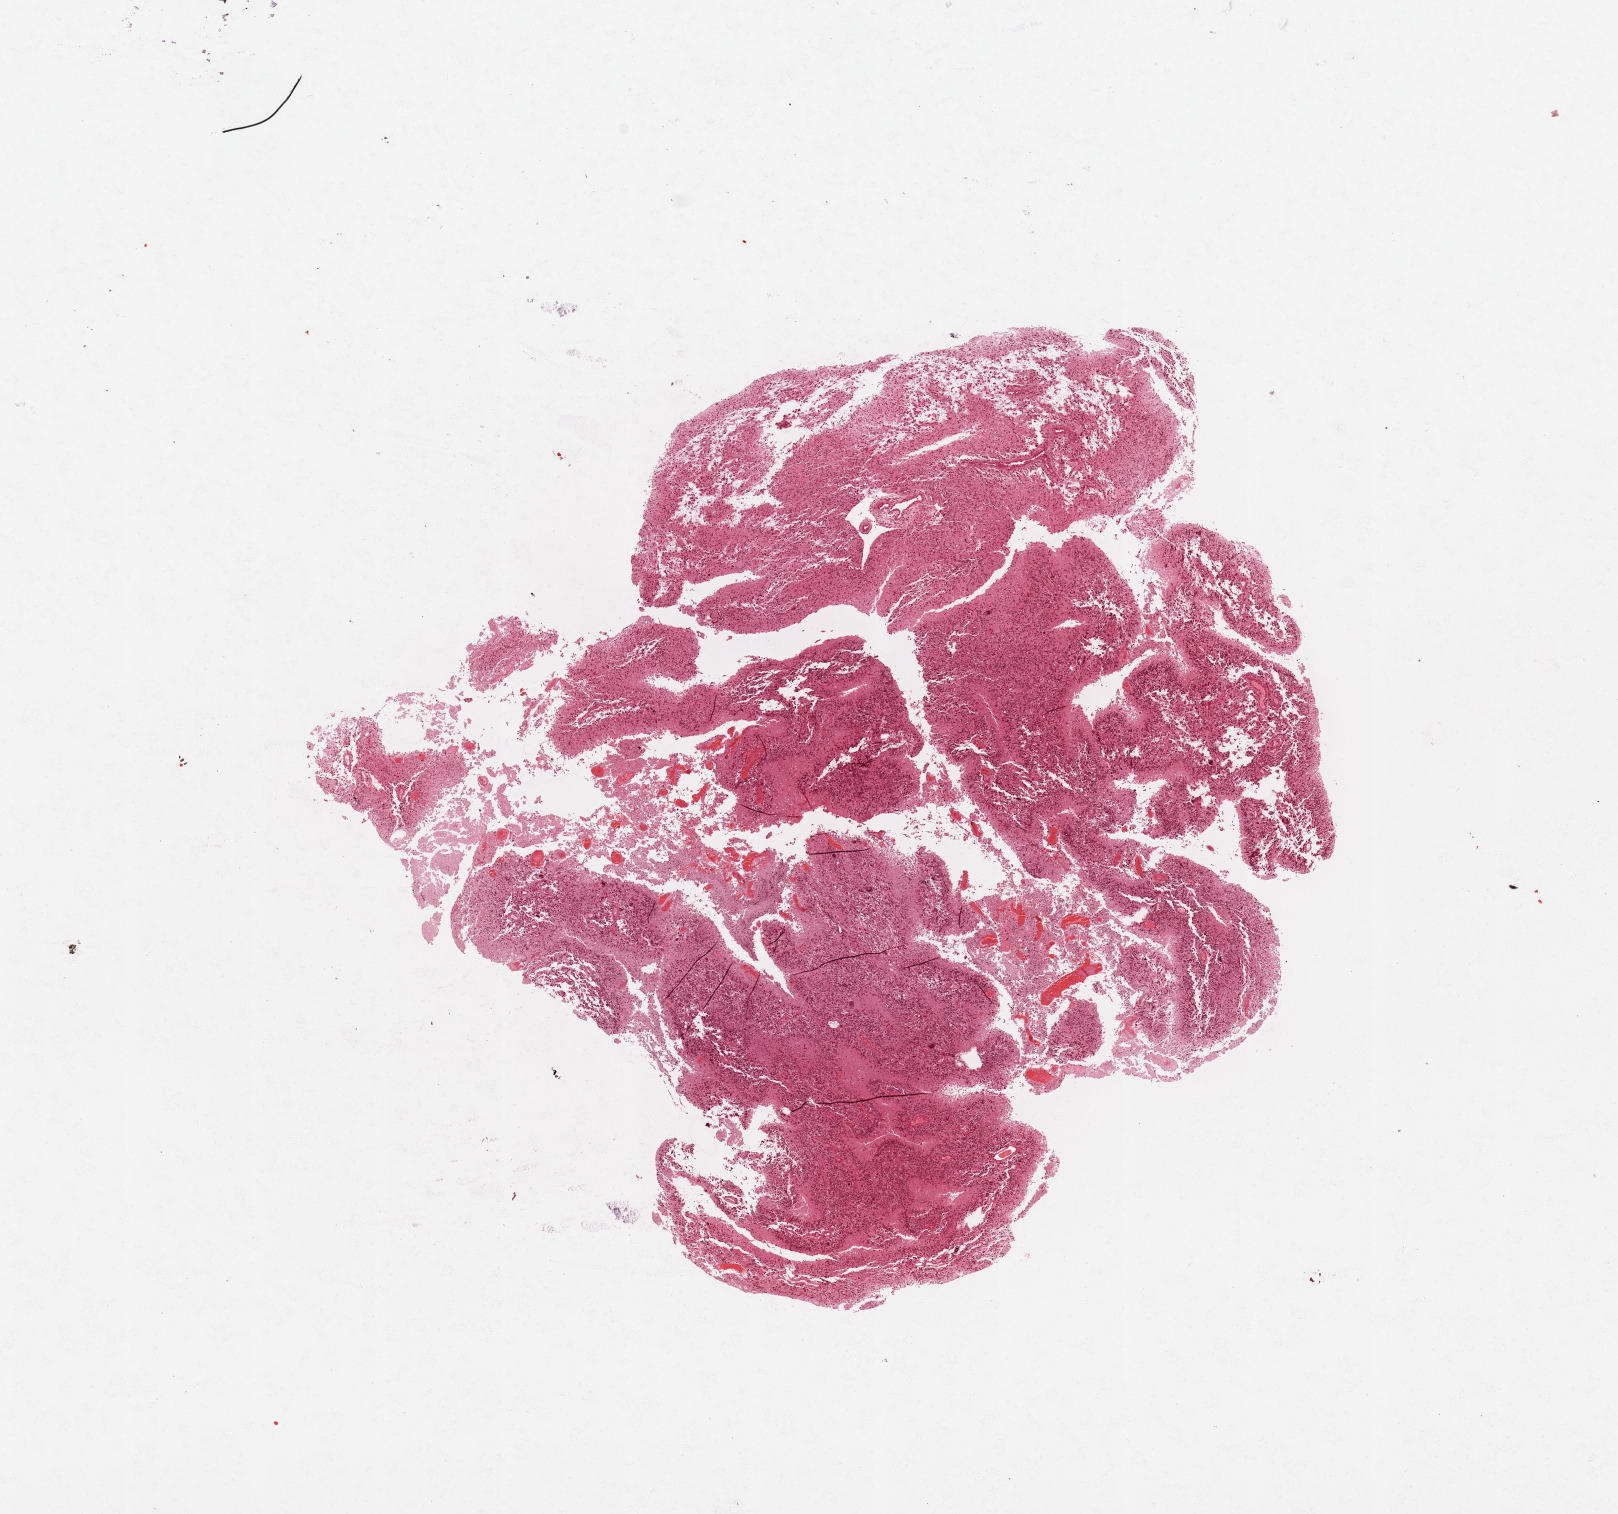
Digitized H&E tissue section (whole slide) — a low-resolution overview of the entire scanned area, about 12.8 x 12.0 mm (slide scanned at 20x); tumour tissue sample, brain. 48-year-old female patient.
Histologic diagnosis: Glioblastoma.